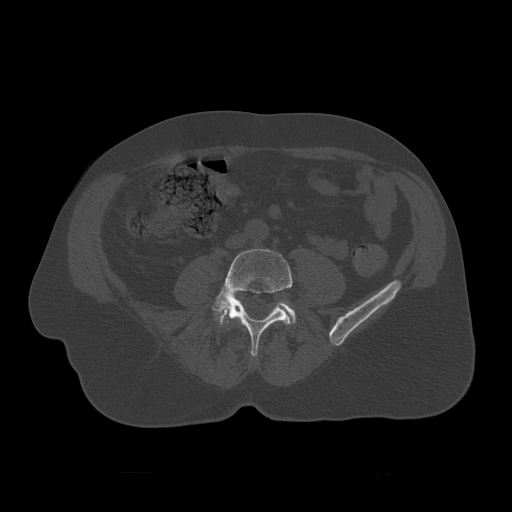
CT including the spine, one axial slice; slice 275 of 450 in the series (ordered by position); 120 kVp; bone window (W 1800 / L 400 HU); 512 × 512 image matrix, field of view 405 × 405 mm. Patient age 75 years. From the clinical record (not read from this slice): primary cancer: prostate.
Structures marked on this image (semi-automatically segmented with operator editing):
- L4 vertebra: bounding box <212,249,293,357> (left, top, right, bottom; pixels)
- L5 vertebra: <215,300,296,326>